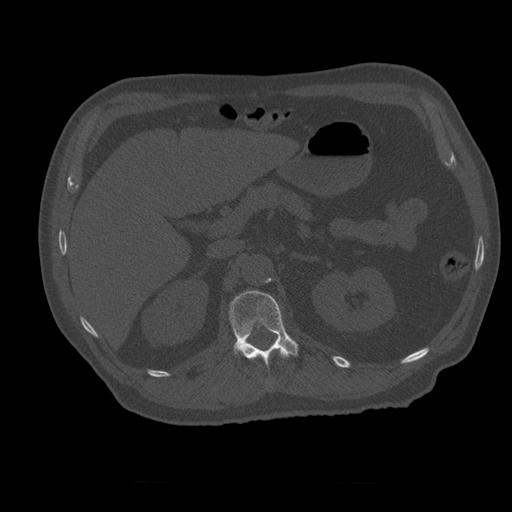
CT including the spine, one axial slice; position 240 of 399 along the scan axis; bone window (W 1800 / L 400 HU); 1.25 mm slice thickness; 512 × 512 image matrix. Patient age 73 years. From the clinical record (not read from this slice): primary cancer: prostate.
Annotated regions visible in this slice (semi-automatically segmented with operator editing):
- L1 vertebra: bounding box [x1, y1, x2, y2] px = [230, 291, 298, 367]
- T12 vertebra: [250, 352, 290, 359]